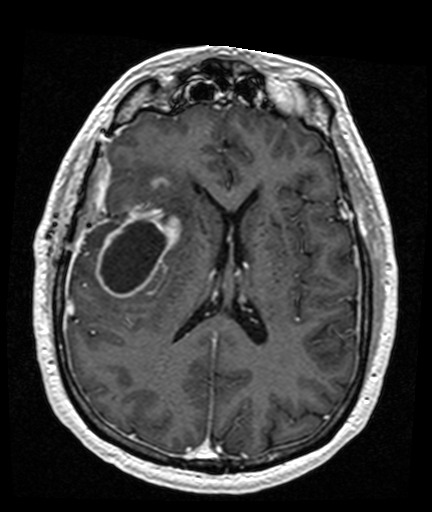
Brain MRI from a brain-tumour surgery series, one axial slice; position 72 of 176 along the scan axis; T1-weighted post-contrast; 1 mm slice thickness; 432 × 512 image matrix, field of view 194 × 230 mm. Case-level facts recorded for this patient, not image findings: histopathology: Glioblastoma; WHO grade: 4; IDH mutation: no; tumour location: Right Frontal Temporal, Posterior Sylvian Fissure.
Outlined on this slice (expert manual segmentation):
- tumour: bounding box <96,177,179,298> (left, top, right, bottom; pixels)